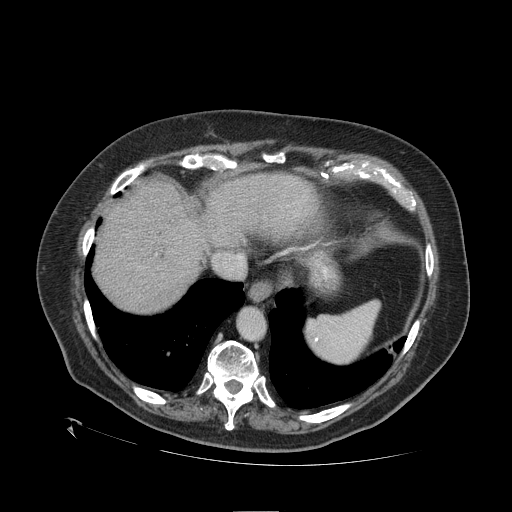
Contrast-enhanced abdominal CT (liver protocol), one axial slice; position 91 of 109 along the scan axis; 120 kVp; one of 2 acquisitions stored at this slice position; soft-tissue window (W 400 / L 40 HU); 512 × 512 image matrix, field of view 460 × 460 mm. Case-level facts recorded for this patient, not image findings: diagnosis: hepatocellular carcinoma (patient treated with transarterial chemoembolisation; whether this scan precedes or follows treatment is not stated here); TNM stage (as recorded): Stage-I; Child-Pugh class: A; tumour differentiation: no biopsy; tumour nodularity: uninodular.
Structures marked on this image (semi-automatically segmented with operator editing):
- abdominal aorta: bounding box <239,309,264,339> (left, top, right, bottom; pixels)
- liver parenchyma outside the tumour (the mass and vessels are separate outlines, so this box may not span the whole liver): <94,174,296,312>